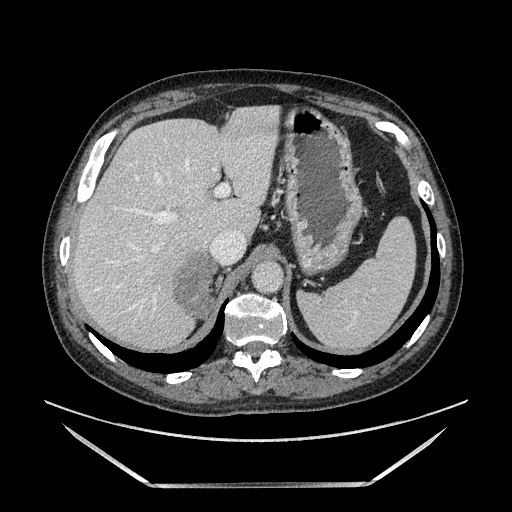
Contrast-enhanced abdominal CT, one axial slice. Position 109 of 185 along the scan axis. Soft-tissue window (W 400 / L 40 HU). 512 × 512 image matrix, field of view 440 × 440 mm. Male patient. Case-level facts recorded for this patient, not image findings: diagnosis: adrenocortical carcinoma; tumour side: right adrenal; tumour size at pathology: 10.3 cm; Ki-67 index: 20 %; stage (as recorded): 3.
Structures marked on this image (semi-automatic segmentation, software-assisted and operator-edited):
- mass: box from (x=176, y=253) to (x=215, y=315) px